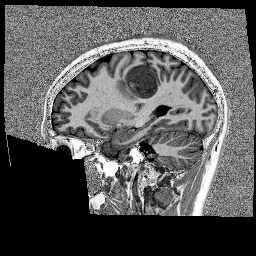
Brain MRI from a brain-tumour surgery series, one sagittal slice; position 64 of 176 along the scan axis; 1 mm slice thickness; 256 × 256 image matrix, field of view 256 × 256 mm. From the clinical record (not read from this slice): histopathology: Glioblastoma; WHO grade: 4; IDH mutation: no; tumour location: Left Frontal.
Annotated regions visible in this slice (outlined manually by an expert reader):
- tumour: bounding box (x1, y1, x2, y2) in pixels: (118, 59, 175, 94)